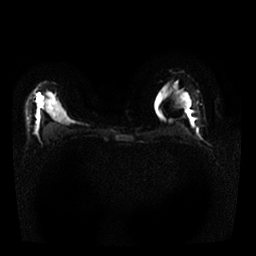
Breast MRI, one axial slice; position 18 of 25 along the scan axis; diffusion-weighted series; image 2 of 4 stored at this slice position (different b-values; order by instance number); 1.5 T; 256 × 256 image matrix, field of view 320 × 320 mm. Female patient.
Annotated regions visible in this slice (expert manual segmentation):
- tumour on diffusion-weighted imaging: bounding box (x1, y1, x2, y2) in pixels: (38, 94, 41, 101)